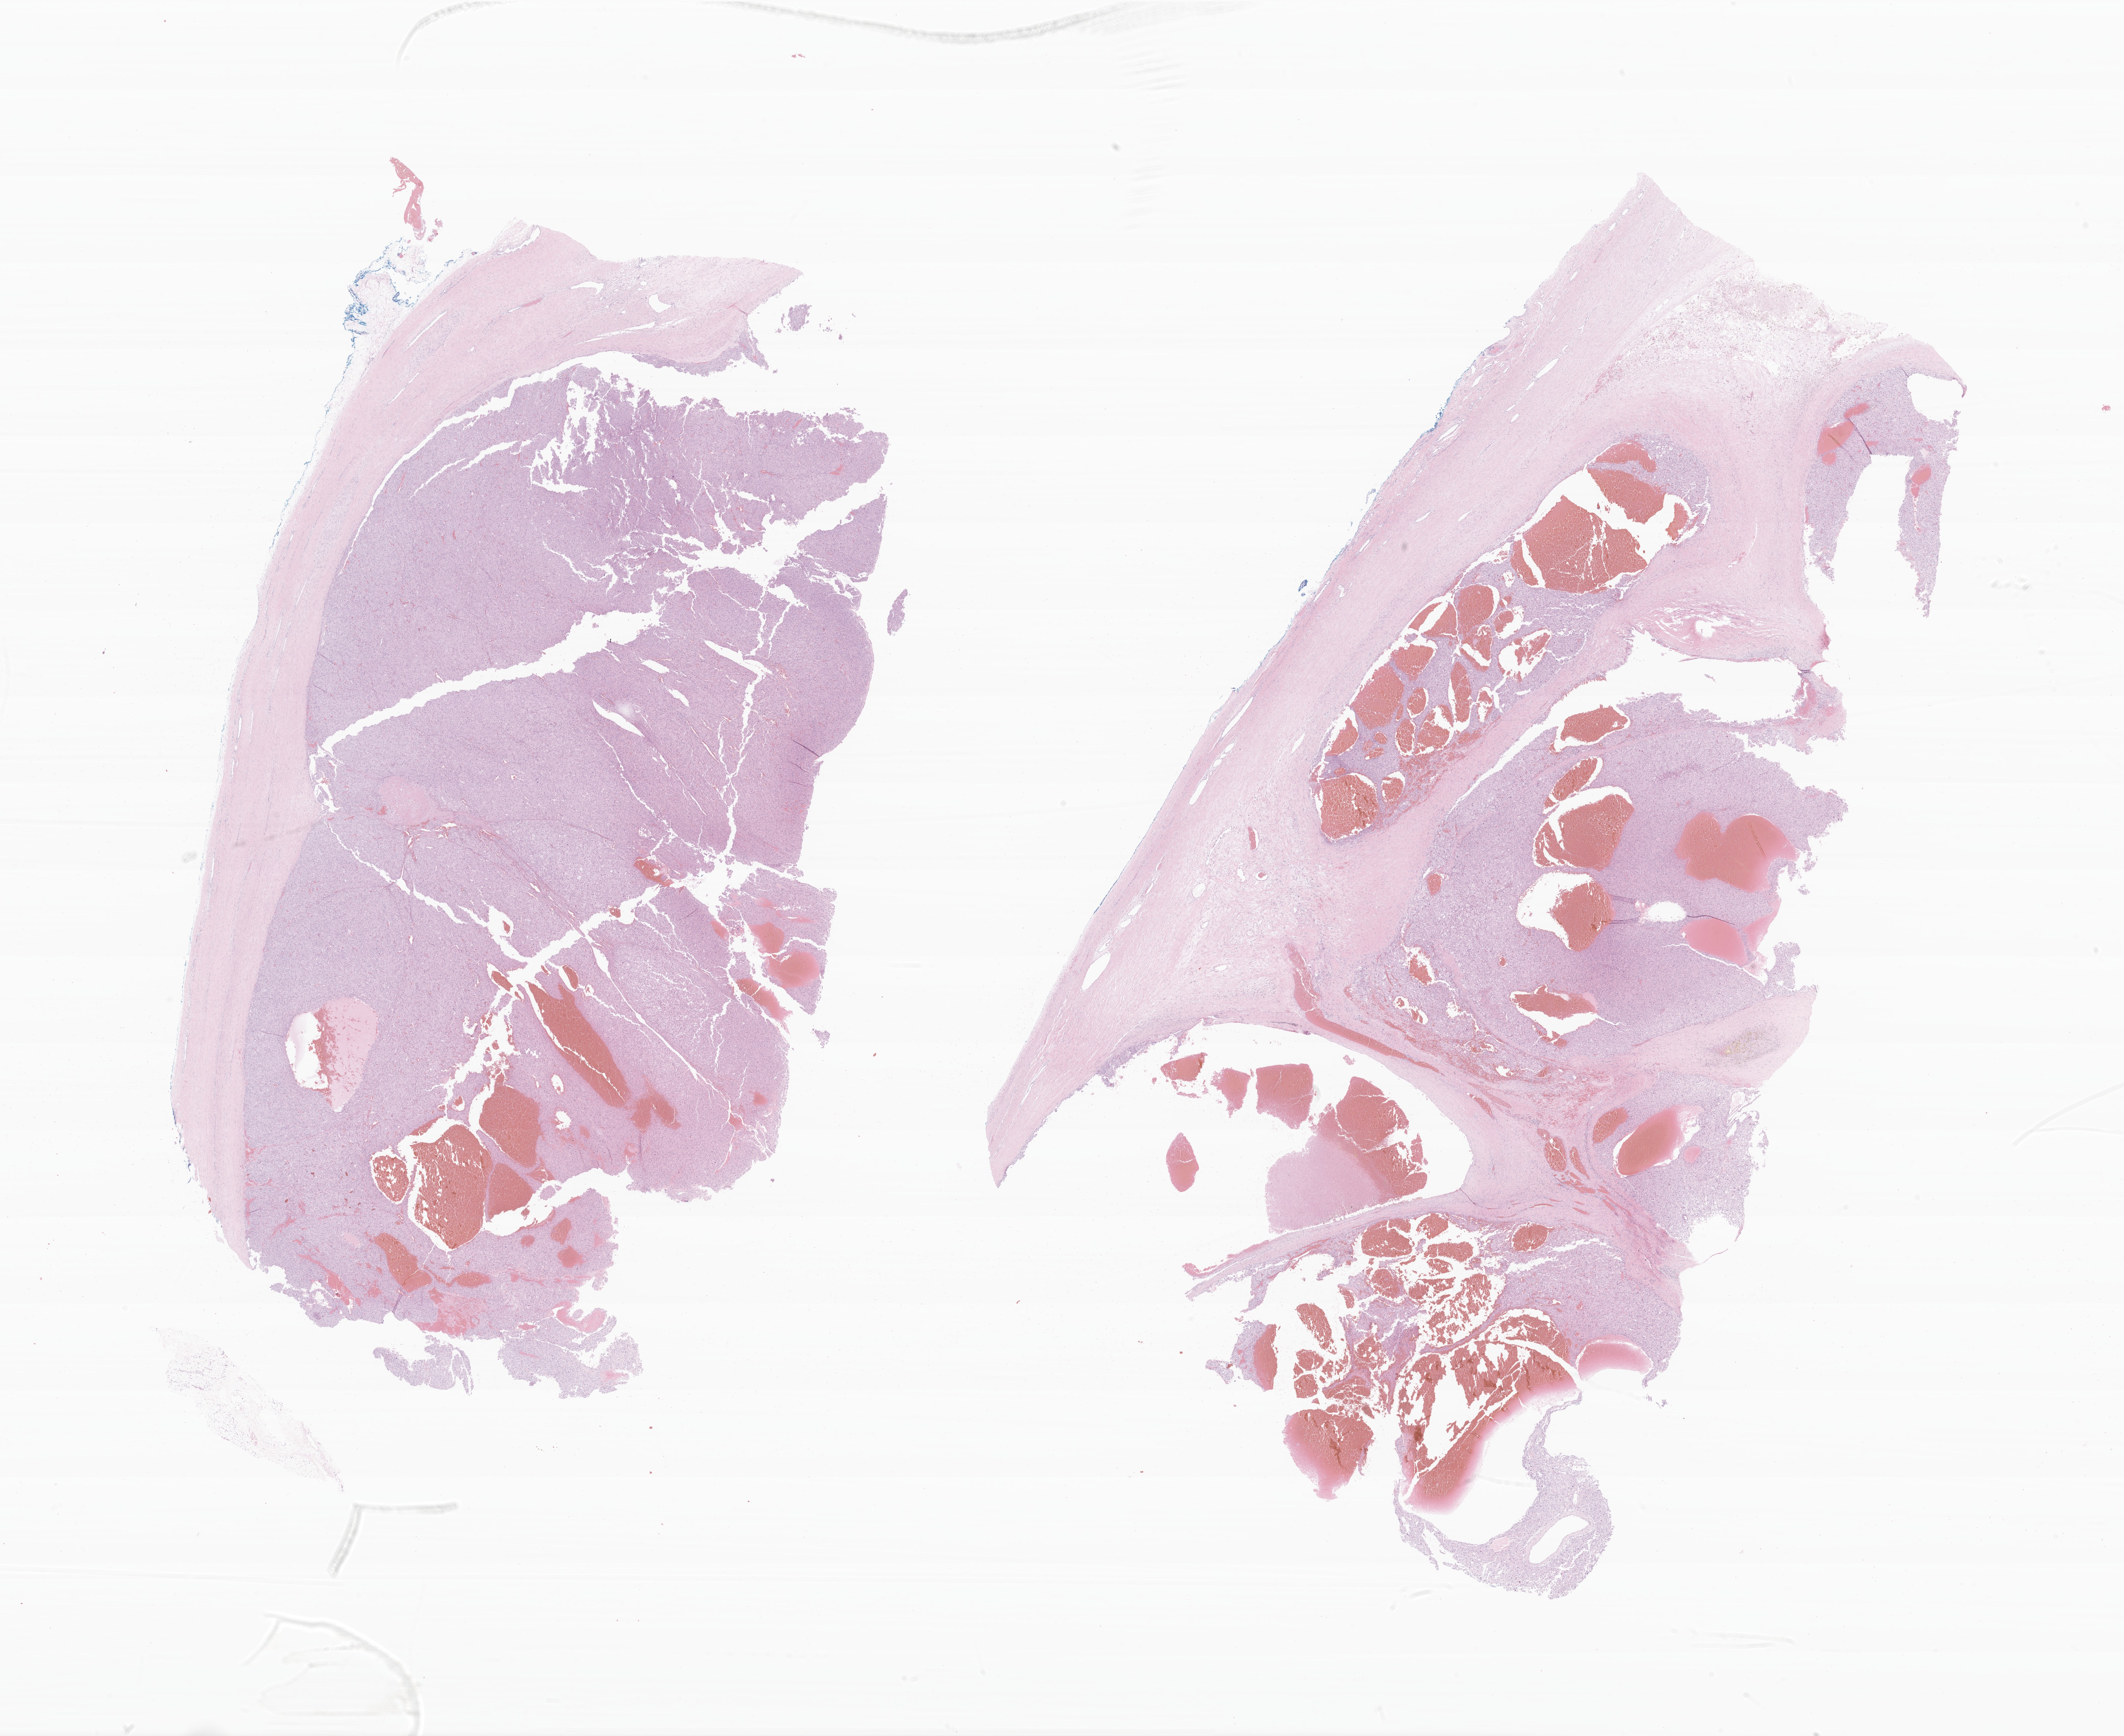
Whole-slide image, H&E stain of tumor tissue from the adrenal cortex, low-resolution overview of the scanned area, about 26.1 x 21.3 mm; formalin-fixed, paraffin-embedded (FFPE) tissue. Patient male; age 39 months (3 years 3 months).
* diagnosis: Adrenal cortical adenoma, NOS
* tissue or organ of origin (case record): cortex of adrenal gland